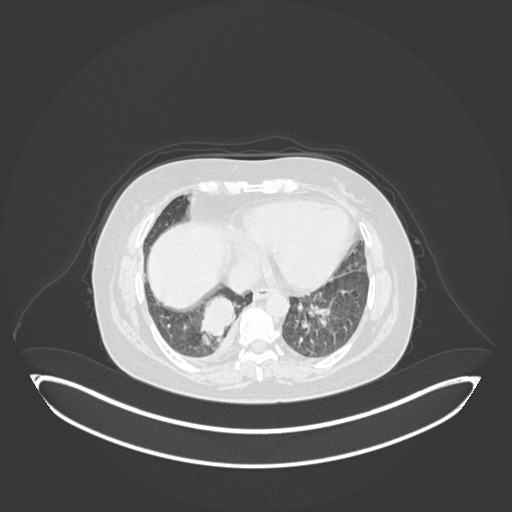
Chest CT, one axial slice; position 44 of 231 along the scan axis; reconstruction kernel B30f; lung window (W 1500 / L -600 HU); 1 mm slice thickness; 512 × 512 image matrix, field of view 500 × 500 mm. Patient: female, 56 years. Case-level facts recorded for this patient, not image findings: clinical TNM (as recorded): T2b N1 M0; histopathological grade: G3.
Outlined on this slice (bounding box drawn by a radiologist):
- lung tumour (recorded histology: small cell carcinoma): bounding box <195,286,243,339> (left, top, right, bottom; pixels)